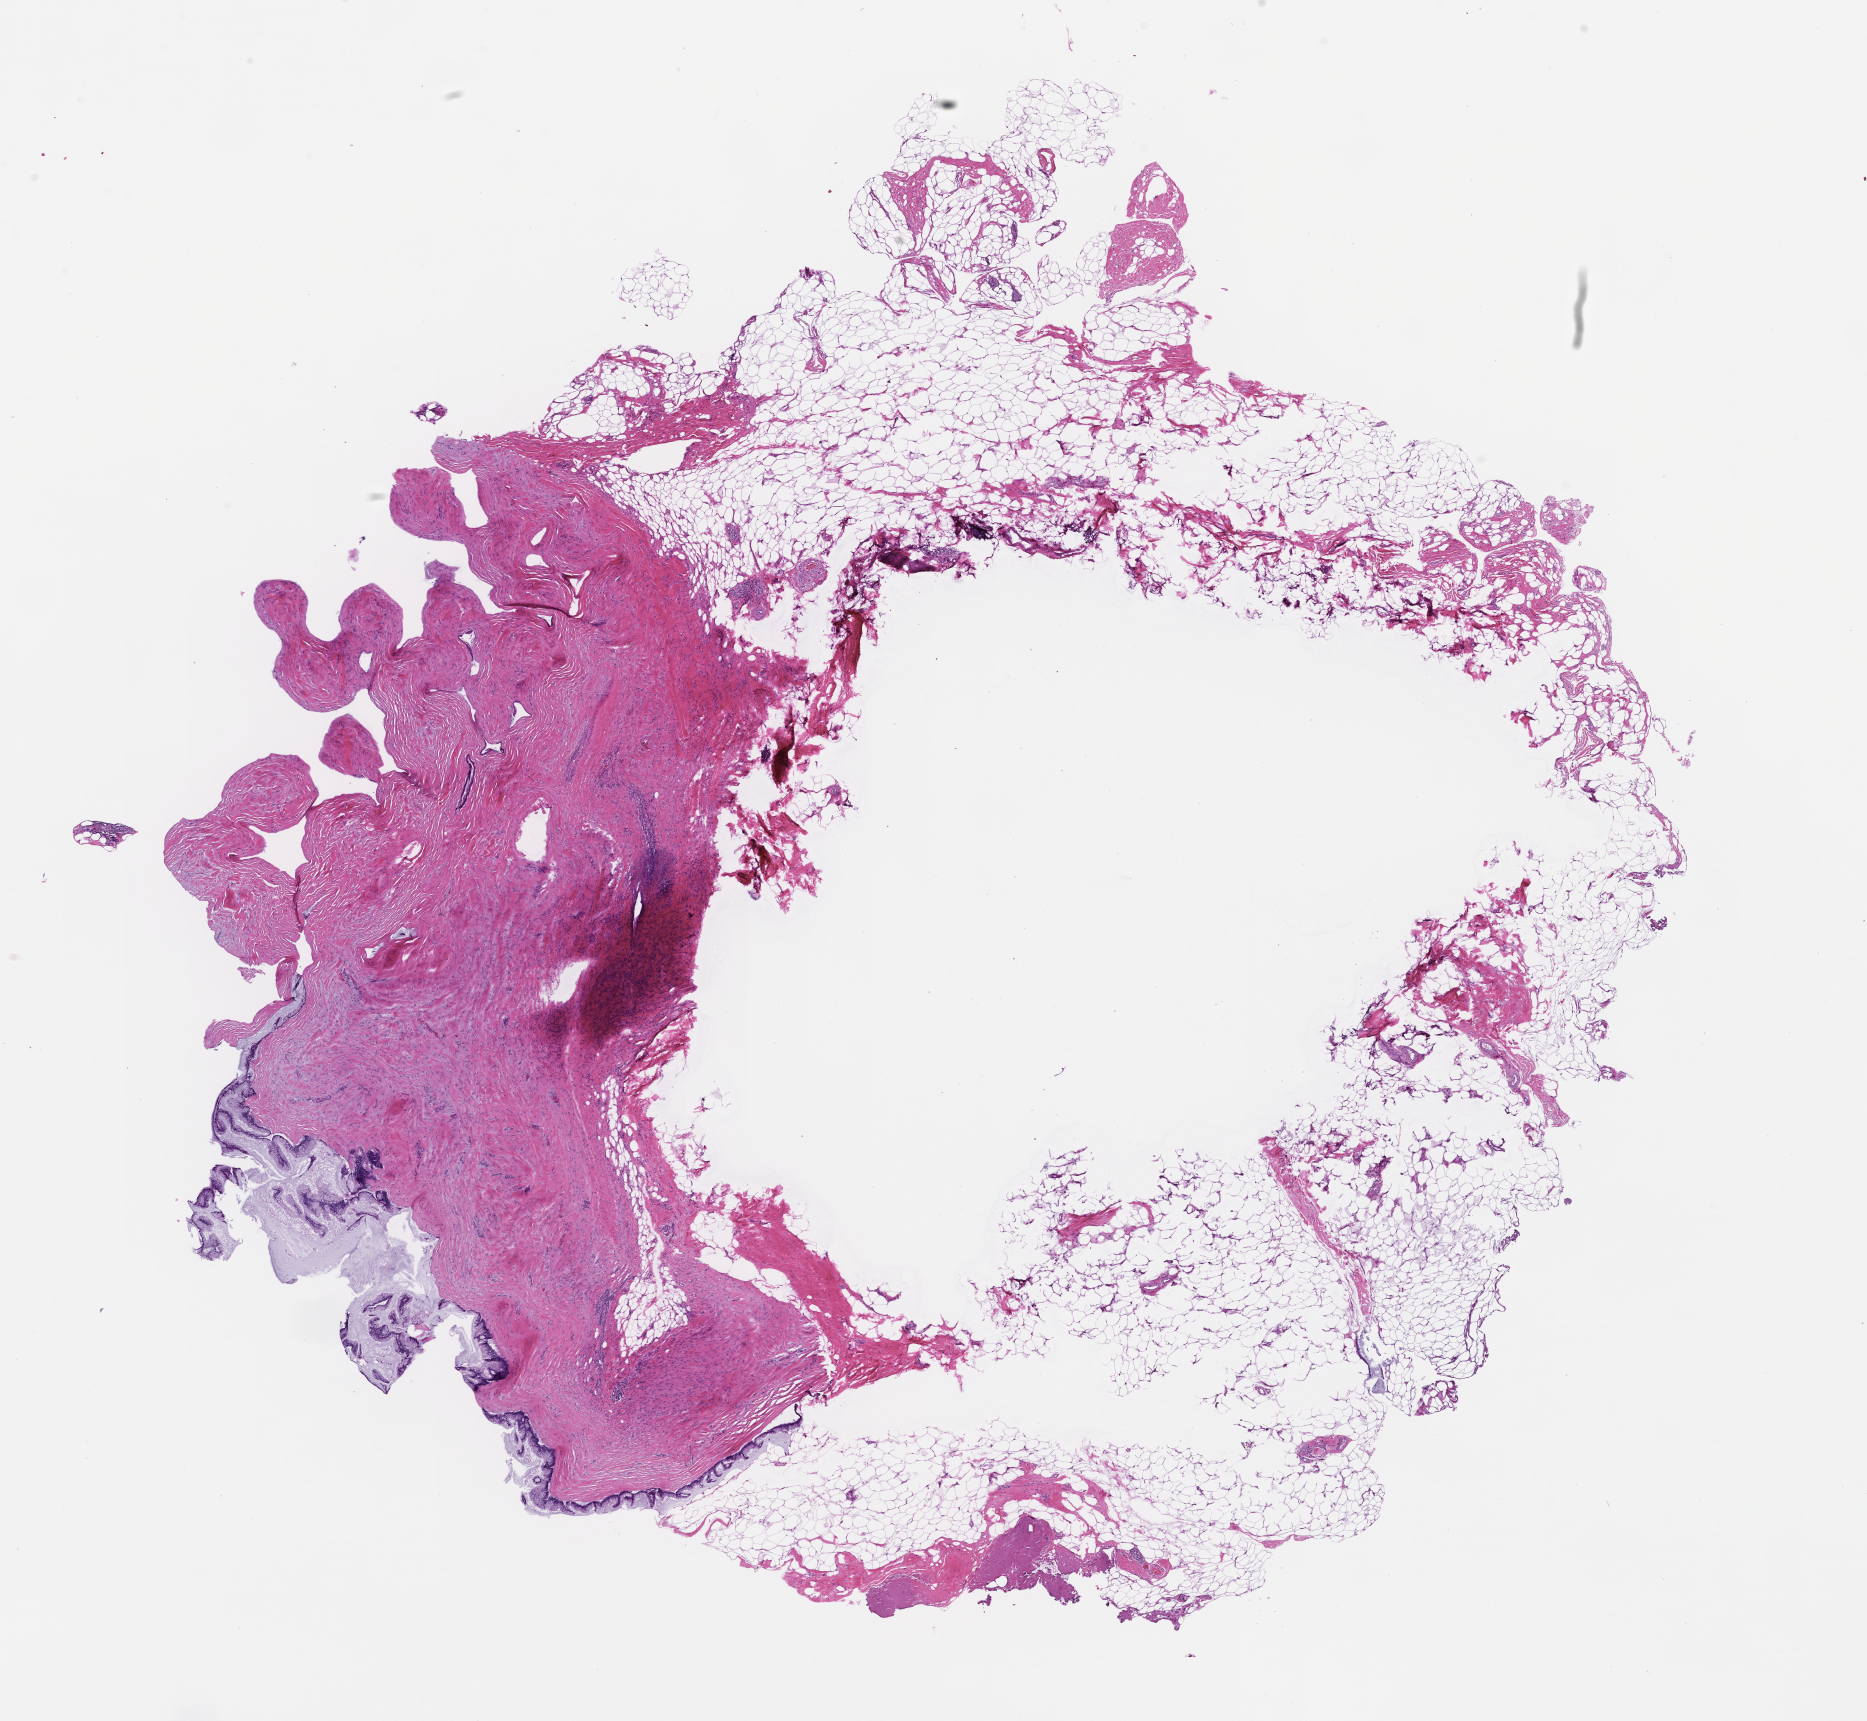
Digitized H&E-stained section, low-resolution overview of the scanned area, about 15.1 x 13.9 mm. Formalin-fixed, paraffin-embedded (FFPE) tissue. Collected at baseline (before treatment). Patient sex: male.
- this section: metastatic tumor tissue
- primary diagnosis of the patient: Colorectal Carcinoma